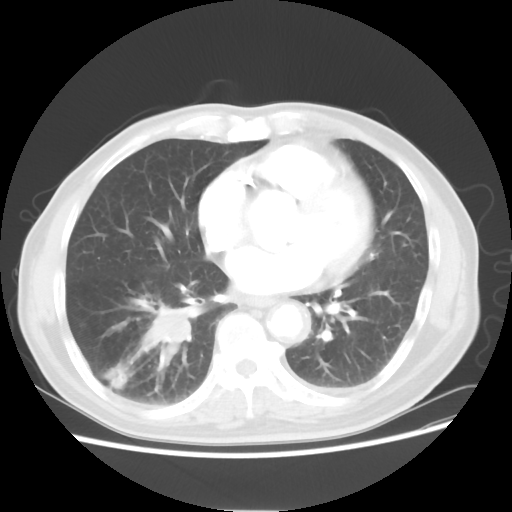
Chest CT, one axial slice. Slice 25 of 58 in the series (ordered by position). Reconstruction kernel STANDARD. 120 kVp. Lung window (W 1500 / L -600 HU). 5 mm slice thickness. 512 × 512 image matrix. Patient: male, 74 years. Case-level facts recorded for this patient, not image findings: clinical TNM (as recorded): T1c N1 M1.
Annotated regions visible in this slice (bounding box drawn by a radiologist):
- lung tumour (recorded histology: adenocarcinoma): bounding box <136,291,203,374> (left, top, right, bottom; pixels)